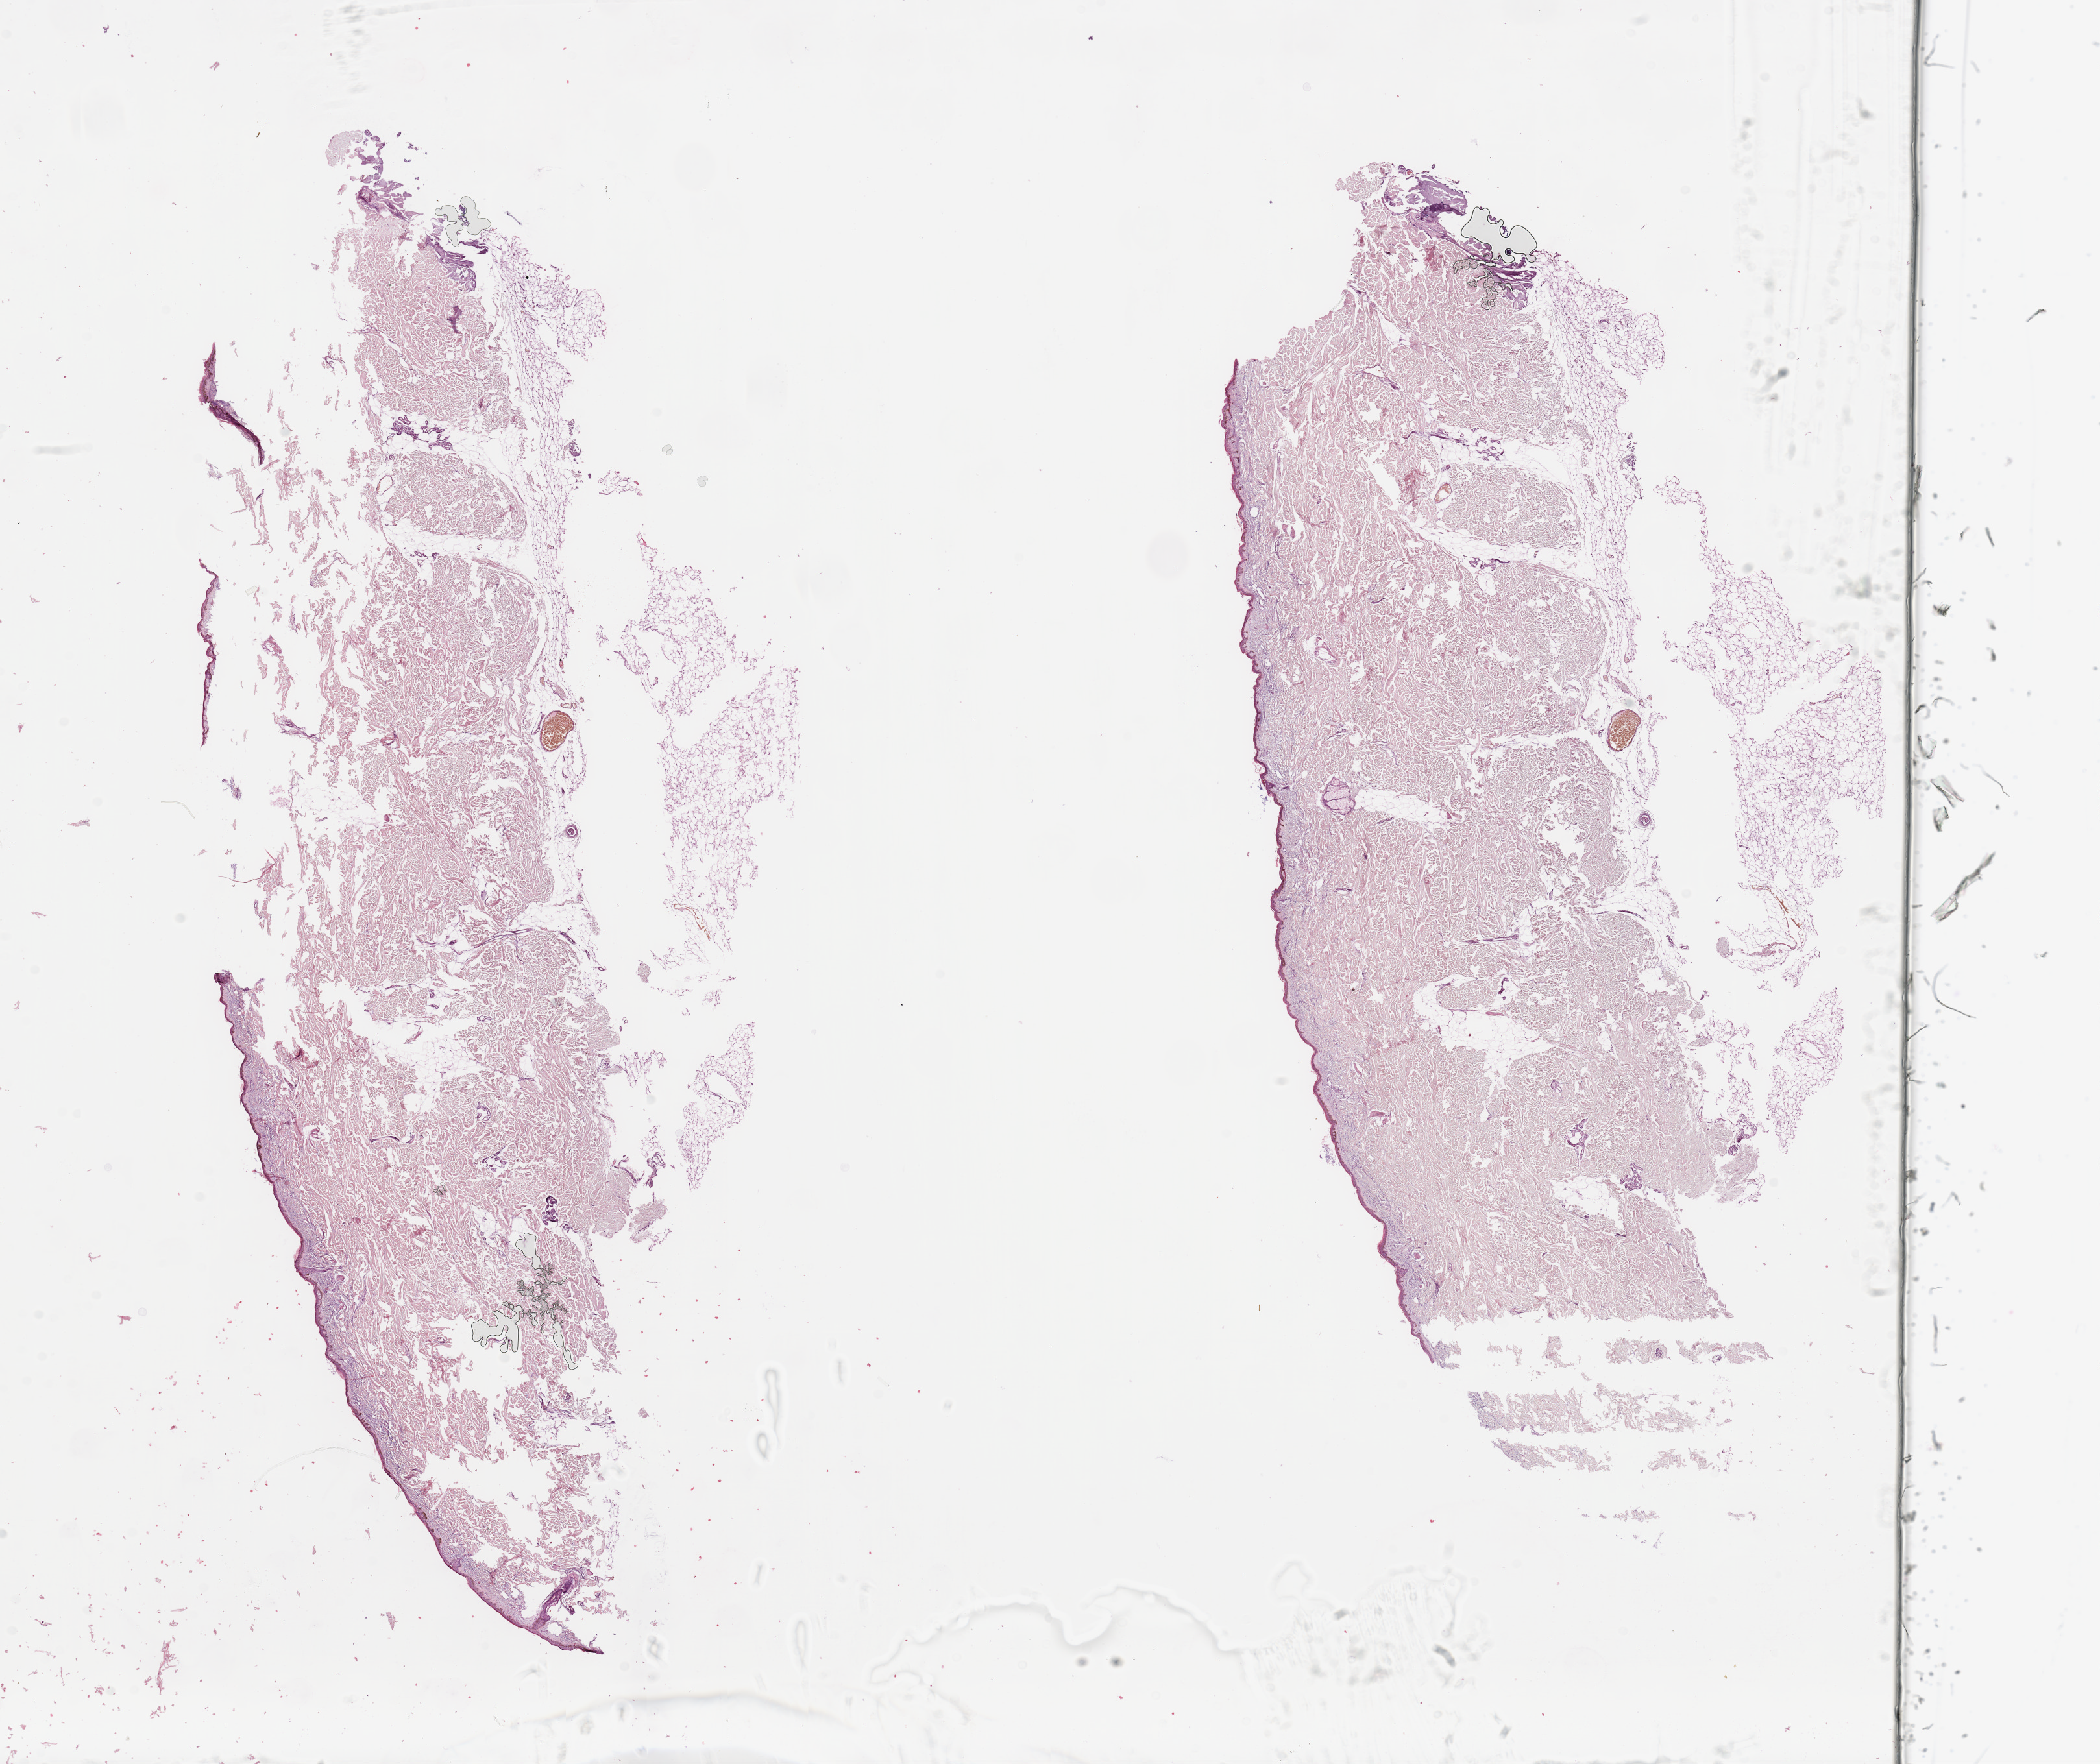
Whole-slide histology image, H&E — shown as a low-resolution overview of the whole scanned area (about 25.6 x 21.5 mm). Normal (non-tumour) tissue sample, sampled site: trunk. 86-year-old female patient.
* this section: normal (non-tumour) tissue from the same patient
* patient diagnosis: Malignant melanoma, NOS